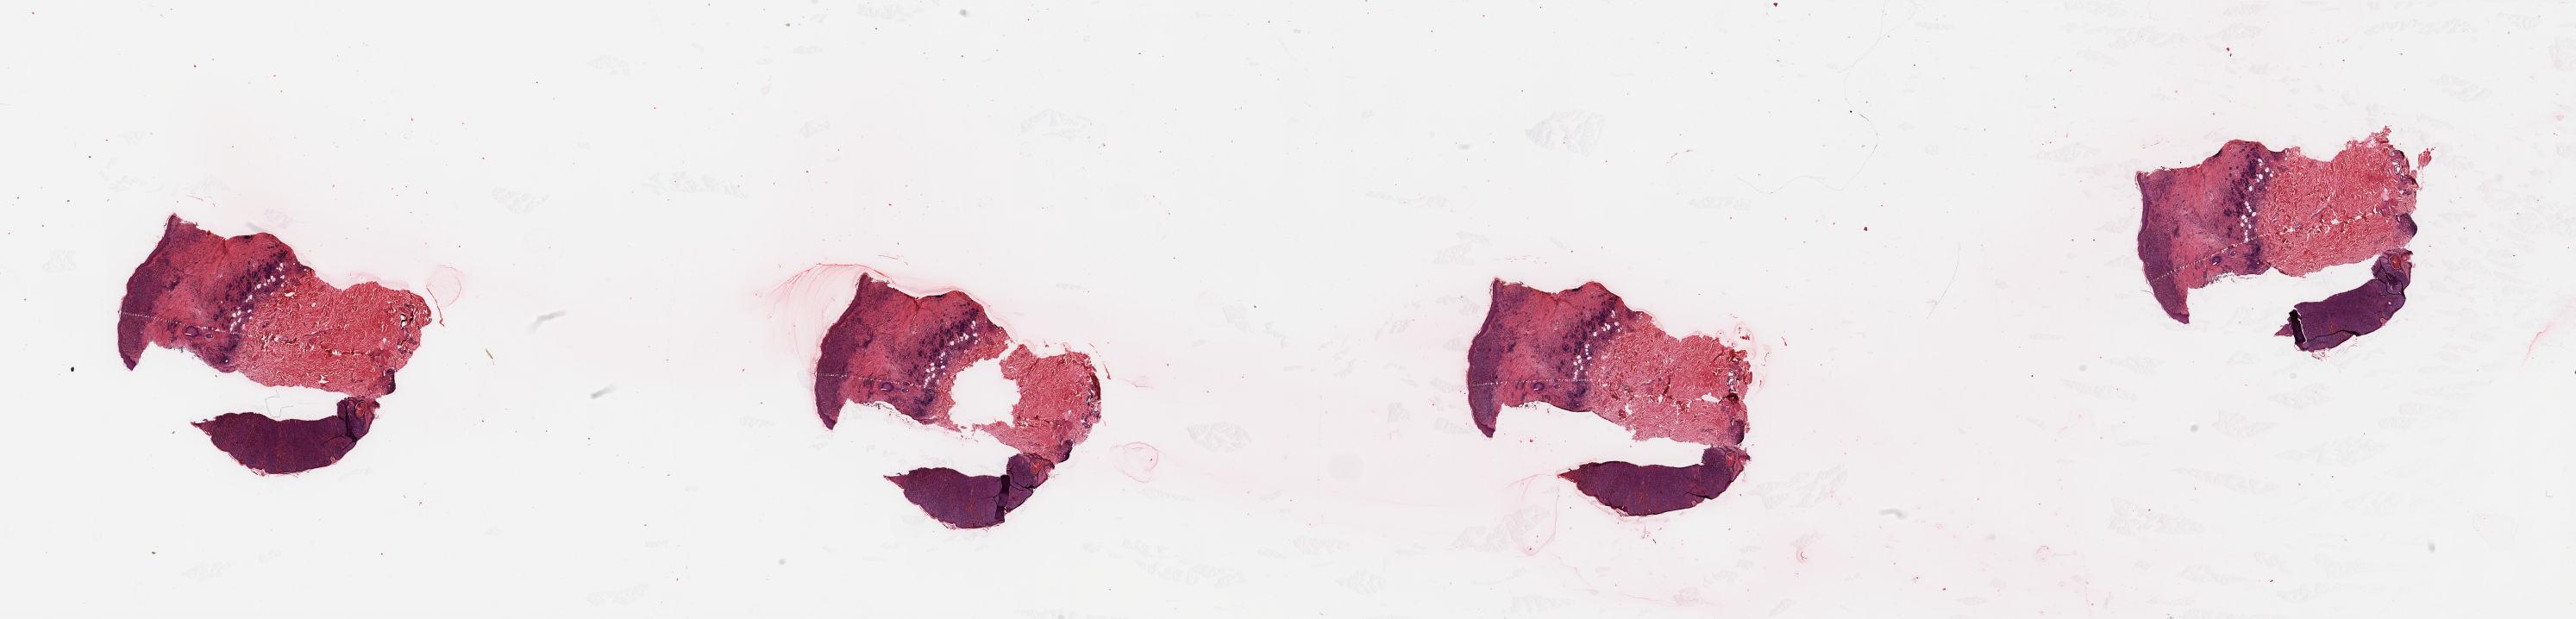
Whole-slide histology image, H&E — shown as a low-resolution overview of the whole scanned area (about 47.3 x 11.4 mm, acquisition: 20x scan); tumour tissue sample, sampled site: trunk. Male, 69 y/o. Composition of this section per pathologist review: tumour nuclei 80%, necrosis 0%.
Primary tumour site (as recorded): trunk. AJCC pathologic stage: IIA. Diagnosis: Malignant melanoma, NOS.